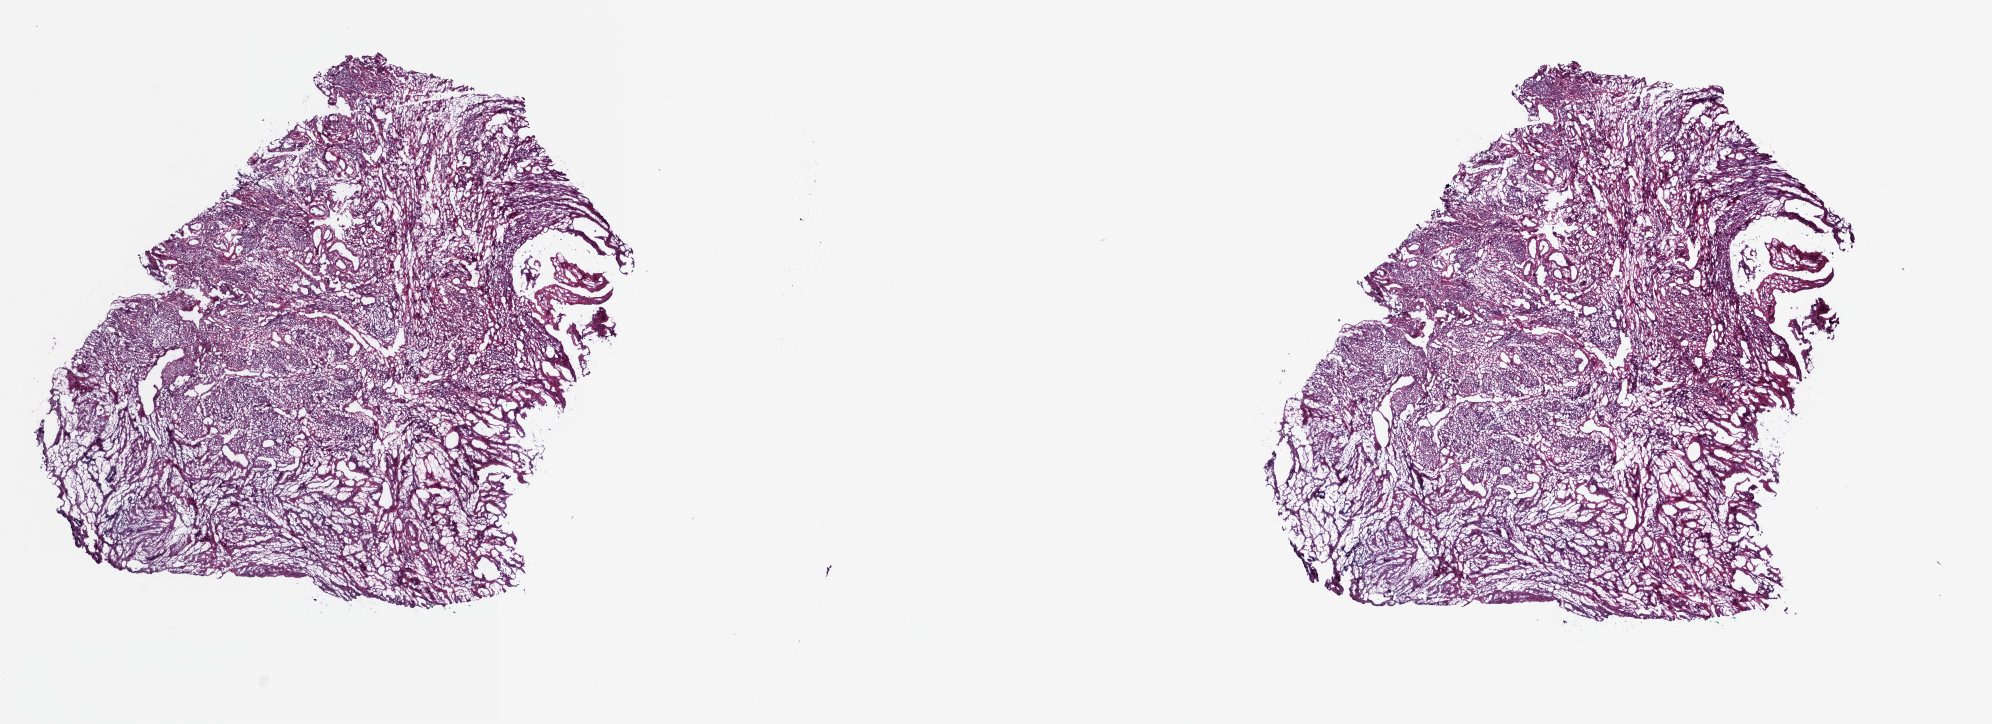
H&E whole-slide image, a low-resolution overview of the entire scanned area, about 15.8 x 5.8 mm (from a 20x scan). Frozen section from the top of the tissue portion. Uterus, solid tissue normal (non-tumour tissue) sample. Composition of this section per pathologist review: tumour cells 0%, normal cells 100%.
- this section: solid tissue normal sample (biorepository sample class)